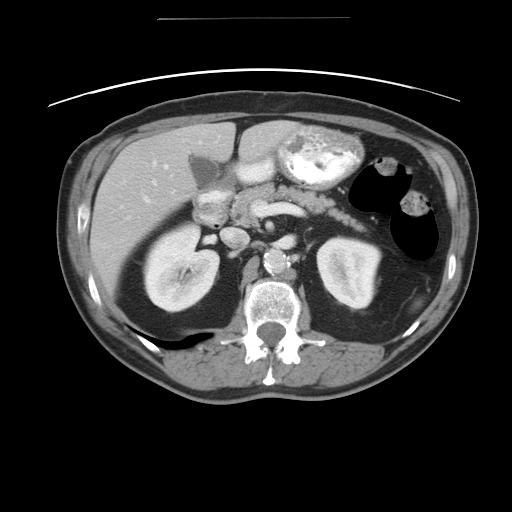
Contrast-enhanced abdominal CT, one axial slice. 120 kVp. Intravenous contrast given. Soft-tissue window (W 400 / L 40 HU). 5 mm slice thickness. 512 × 512 image matrix, field of view 413 × 413 mm. Male patient, age 57 years. Case-level facts recorded for this patient, not image findings: diagnosis: colorectal cancer liver metastases, imaged before liver resection; multiple liver metastases: yes.
Structures marked on this image (manually delineated by an expert):
- hepatic veins: bounding box [x1, y1, x2, y2] px = [152, 141, 200, 183]
- liver: [90, 121, 298, 293]
- planned liver remnant (the part of the liver to remain after resection): [213, 121, 298, 165]
- portal vein (with intrahepatic branches): [143, 163, 167, 201]